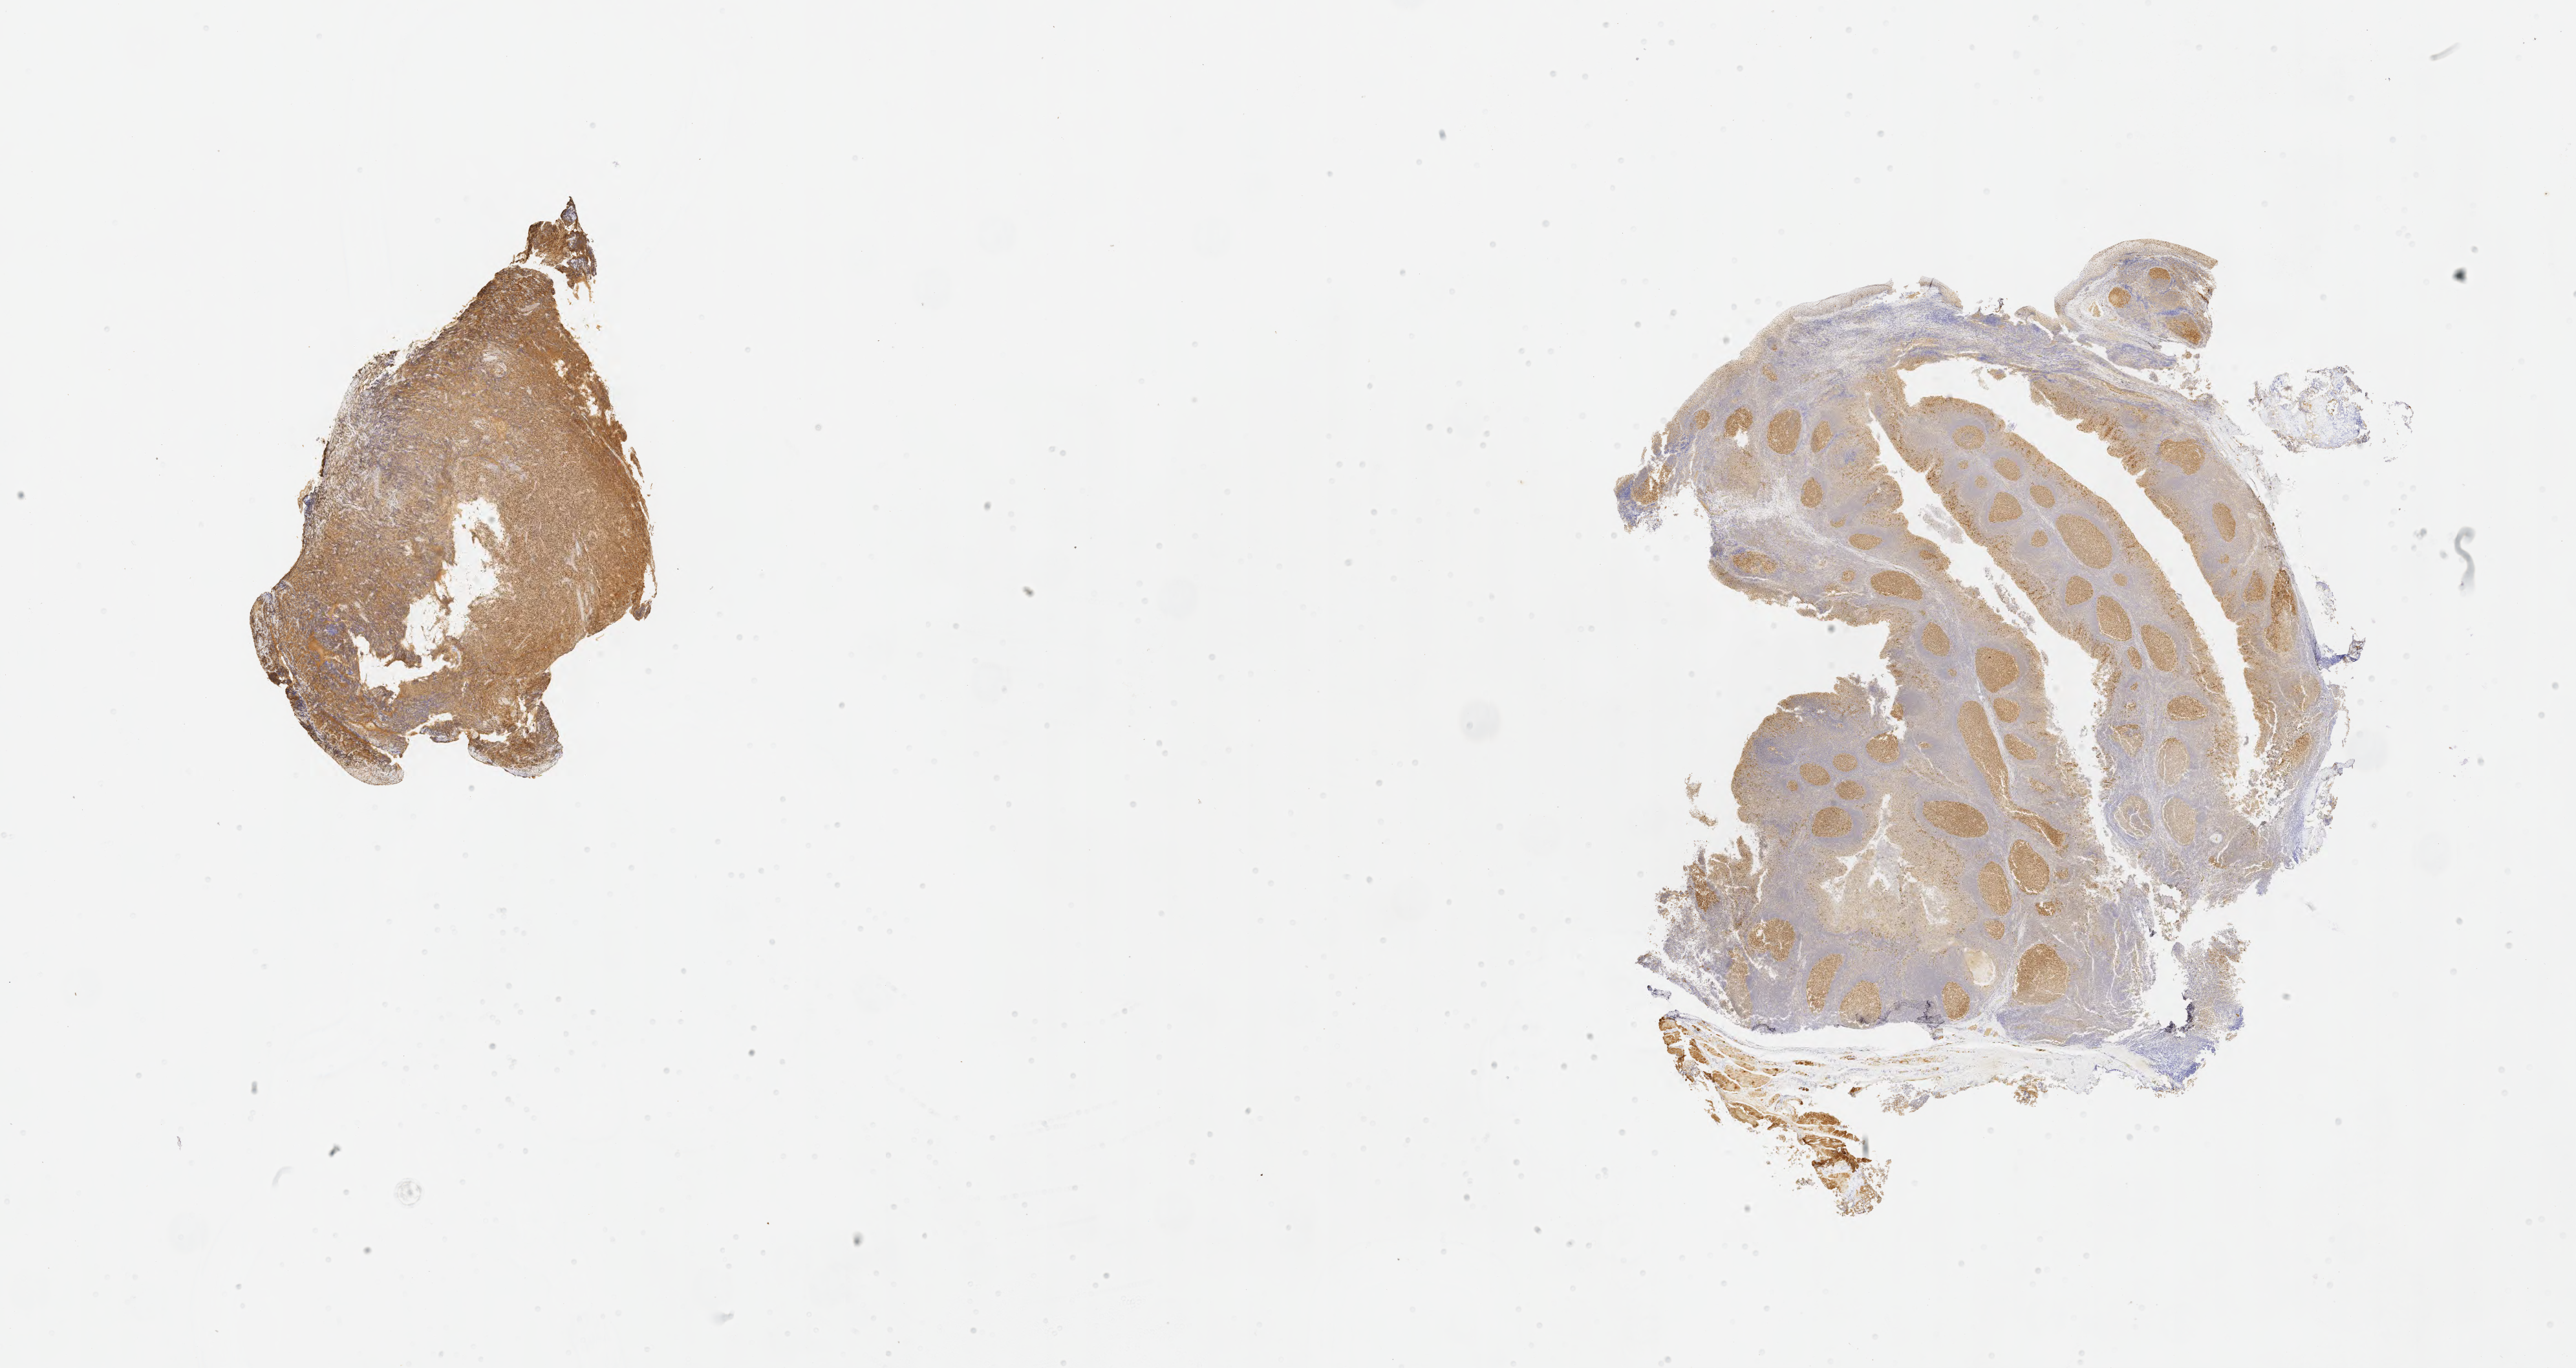
Whole-slide image, immunohistochemical stain for BCL6, whole scanned area (about 32.2 x 17.1 mm) shown as a low-resolution overview. Specimen: tumor tissue. Site: ovary. Female, age 3 years at initial diagnosis.
Diagnosis: Burkitt lymphoma, NOS.